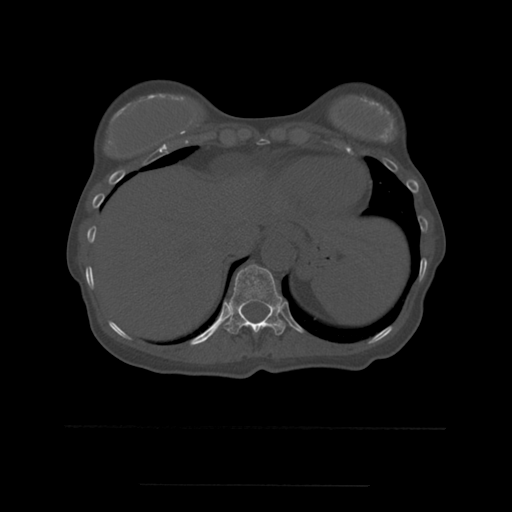
CT including the spine, one axial slice. Slice 285 of 544 in the series (ordered by position). Bone window (W 1800 / L 400 HU). 1.25 mm slice thickness. 512 × 512 image matrix. Patient age 58 years. Case-level facts recorded for this patient, not image findings: primary cancer: lung.
Outlined on this slice (semi-automatically segmented with operator editing):
- T11 vertebra: bounding box (x1, y1, x2, y2) in pixels: (224, 265, 286, 336)